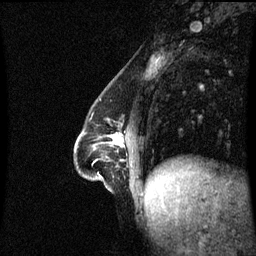
Breast MRI (dynamic contrast-enhanced), one sagittal slice; position 25 of 60 along the scan axis; dynamic contrast-enhanced series, image 2 of 3 at this slice position (ordered by acquisition); 1.5 T; TE 4.2 ms, TR 8.9 ms; 2.2 mm slice thickness; 256 × 256 image matrix, field of view 210 × 210 mm. Female patient, age 47 years. From the clinical record (not read from this slice): setting: breast cancer imaged before/during neoadjuvant chemotherapy; receptor status: HR-positive, HER2-negative.
Annotated regions visible in this slice (semi-automatically segmented with operator editing):
- analysis volume of interest (the breast-tissue region the enhancement analysis was run in; not a lesion): box from (x=75, y=123) to (x=123, y=191) px
- tumour enhancement mask (voxels above the 70 % enhancement threshold inside the analysis volume of interest): (x=113, y=136)–(x=122, y=145)